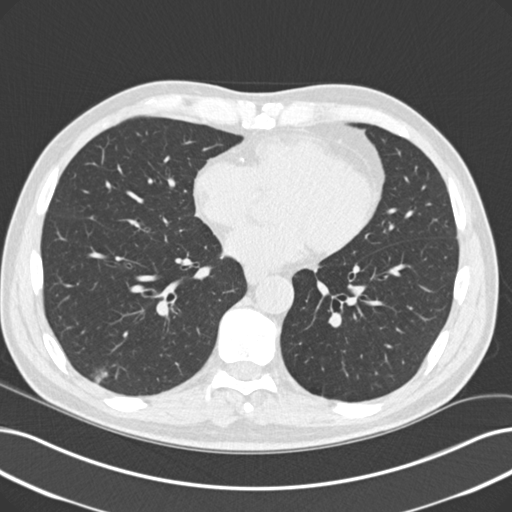
Axial slice from a low-dose chest CT screening exam, baseline screening round, lung window (W 1500 / L -600 HU), 2 mm slice thickness, standard (soft-tissue) reconstruction kernel (B30f), slice 134 of 229 in the series, 512 × 512 image matrix. Male, age 60 years at enrolment. Former smoker at enrolment.
Expert-annotated lung lesion, box from (x=75, y=357) to (x=122, y=403) px. The screening reader recorded 2 non-calcified nodules or masses ≥4 mm on this exam; which of them this box marks is not recorded. Official screen result: positive, change unspecified: nodule(s) >= 4 mm or enlarging nodule(s), mass(es), or other non-specific abnormalities suspicious for lung cancer. Later outcome: lung cancer diagnosed 64 days after this screen — acinar cell carcinoma, right lower lobe, moderately differentiated (G2), stage IA (AJCC 6th edition), 16 mm at pathology.